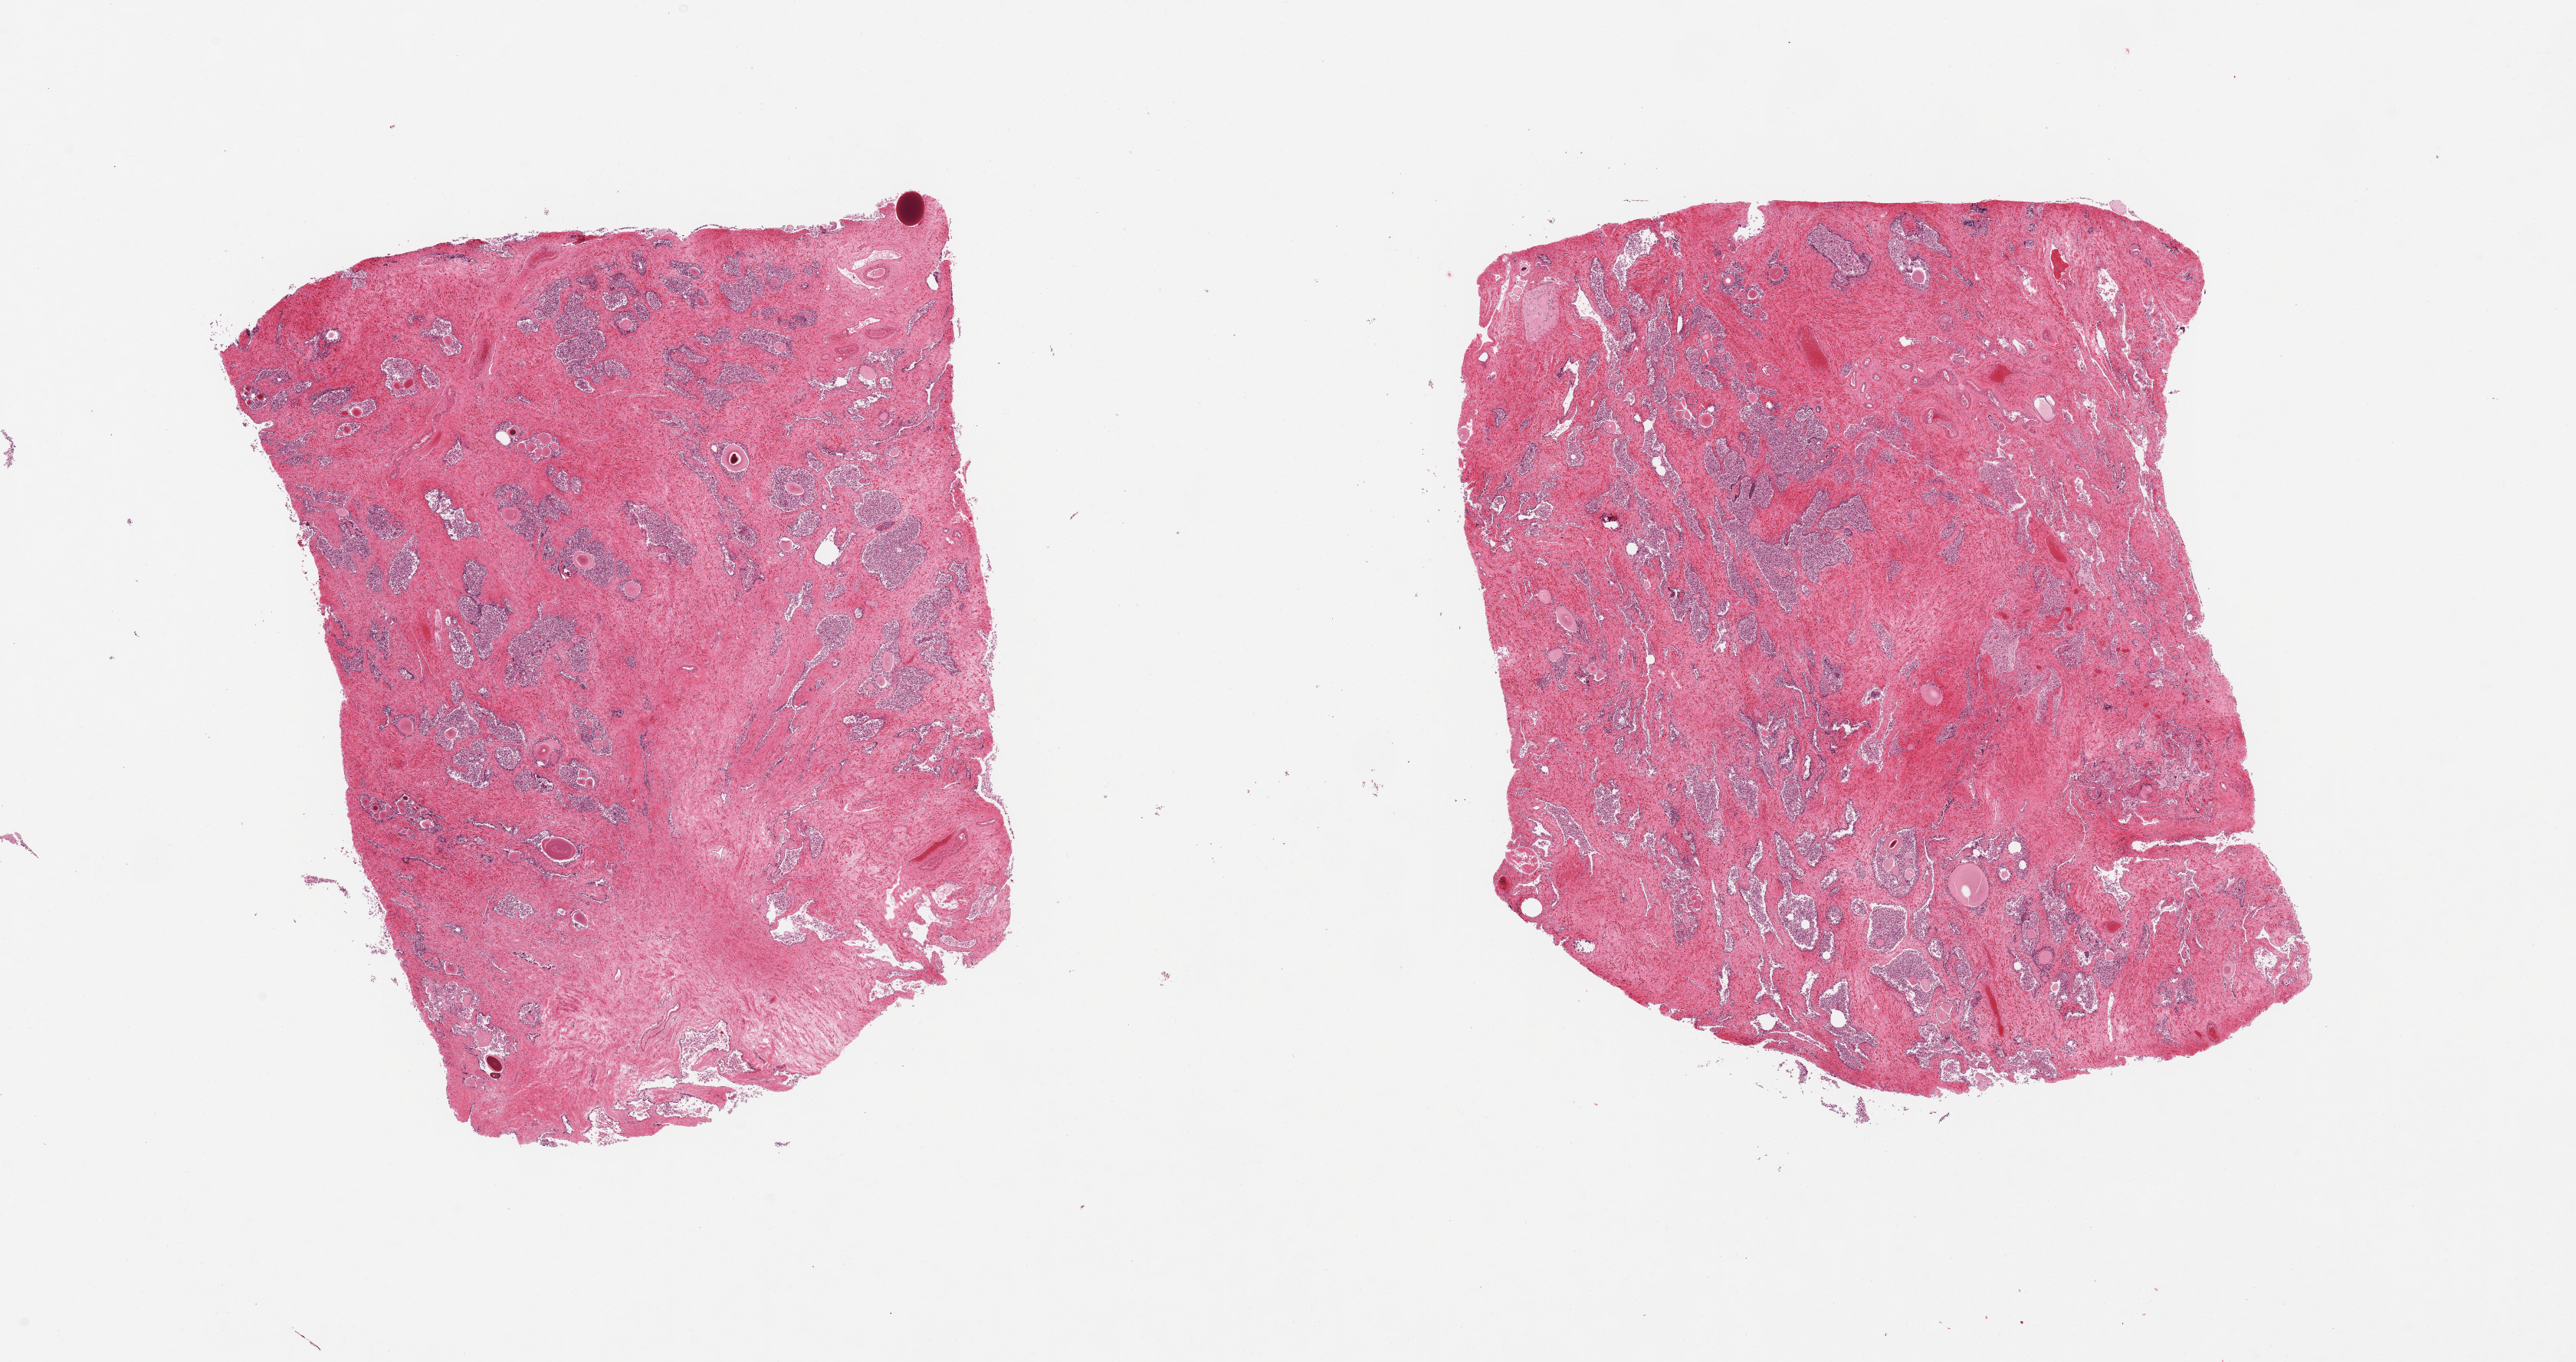
Whole-slide image, H&E stain — a low-resolution overview of the entire scanned area, about 26.6 x 14.1 mm; PAXgene-fixed, paraffin-embedded tissue; sampled site (target tissue): prostate; tissue donor sample. Donor sex: male.
- pathologist's review note for this sample: 2 pieces; fibromuscular stroma with sloughed glandular component and corpora amylacea